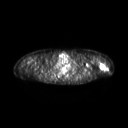
FDG PET of an extremity soft-tissue mass (from a PET/CT study), one axial slice; position 203 of 267 along the scan axis; 3.27 mm slice thickness; 128 × 128 image matrix. Female patient, age 28 years. From the clinical record (not read from this slice): histological type: malignant fibrous histiocytoma; grade: low; site of the primary tumour: left arm.
Outlined on this slice (expert contour drawn on MRI and transferred to this co-registered scan by the dataset authors):
- gross tumour volume (mass): bounding box [x1, y1, x2, y2] px = [99, 62, 106, 70]